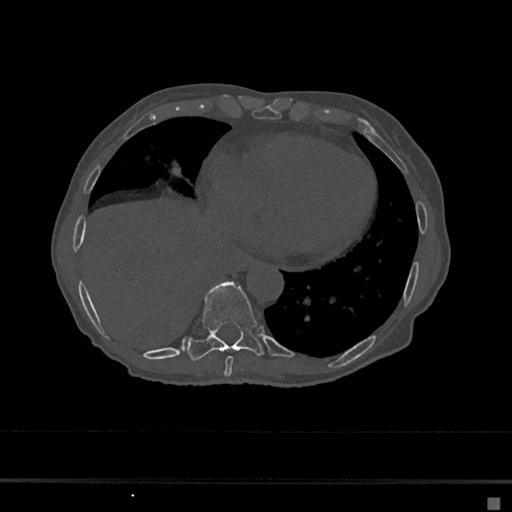
CT including the spine, one axial slice; position 280 of 797 along the scan axis; reconstruction kernel Br40s/3; 120 kVp; bone window (W 1800 / L 400 HU); 512 × 512 image matrix. Female patient, age 68 years. From the clinical record (not read from this slice): primary cancer: renal.
Annotated regions visible in this slice (semi-automatic segmentation, software-assisted and operator-edited):
- T8 vertebra: bounding box <224,356,234,376> (left, top, right, bottom; pixels)
- T9 vertebra: <188,283,263,361>